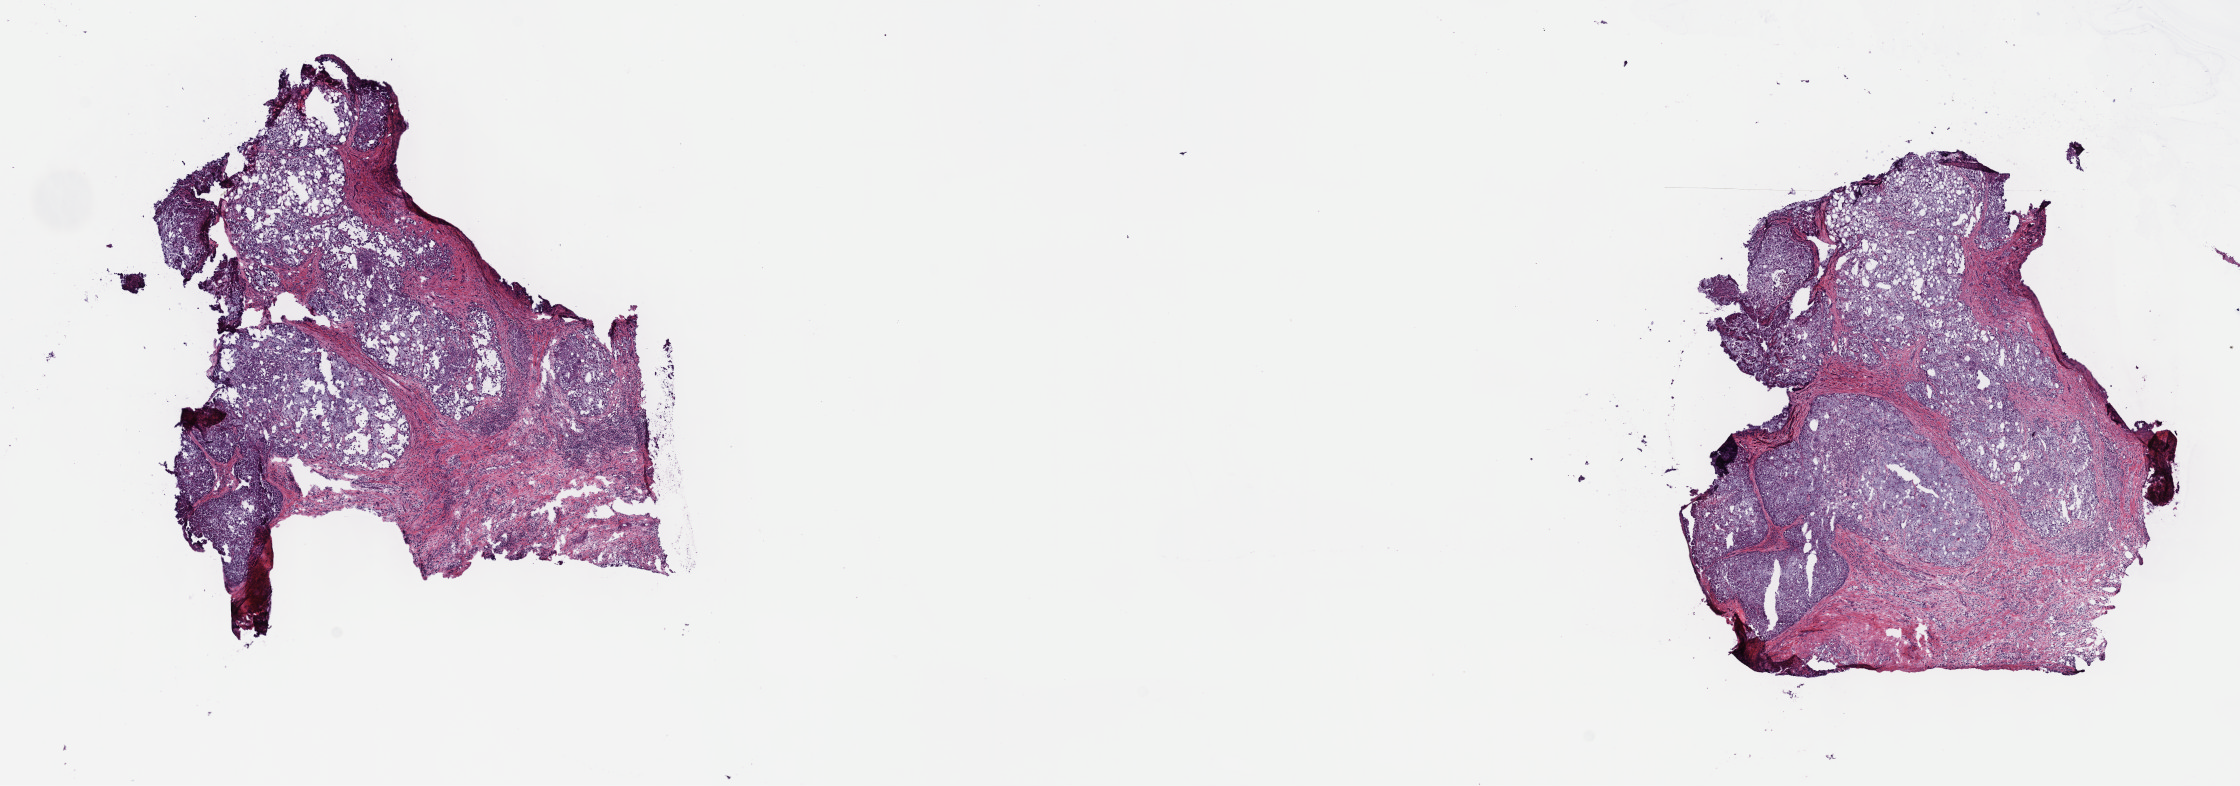
Digitized H&E tissue section (whole slide) — whole scanned area (about 18.1 x 6.4 mm) shown as a low-resolution overview. Frozen section. Primary tumour sample from the liver. Patient: male, age at initial diagnosis 59 years. Histologic grade: G2 (moderately differentiated). Composition of this section per pathologist review: tumour cells 100%, tumour nuclei 60%, normal cells 0%, stromal cells 0%, necrosis 0%. Inflammatory infiltration, as recorded: lymphocyte infiltration 4%, monocyte infiltration 0%, neutrophil infiltration 0%.
* AJCC pathologic stage: I
* histologic diagnosis: Hepatocellular carcinoma, clear cell type